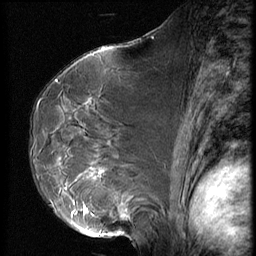
Breast MRI (dynamic contrast-enhanced), one sagittal slice; slice 39 of 62 in the series (ordered by position); 3 images stored at this slice position (order not interpretable as contrast timing); 1.5 T; TE 4.2 ms, TR 9 ms; 2.5 mm slice thickness; 256 × 256 image matrix, field of view 180 × 180 mm. Female patient, age 50 years. From the clinical record (not read from this slice): setting: breast cancer imaged before/during neoadjuvant chemotherapy; receptor status: HR-positive, HER2-negative.
Outlined on this slice (semi-automatically segmented with operator editing):
- analysis volume of interest (the breast-tissue region the enhancement analysis was run in; not a lesion): box from (x=59, y=125) to (x=139, y=238) px
- tumour enhancement mask (voxels above the 140 % enhancement threshold inside the analysis volume of interest): (x=125, y=214)–(x=129, y=217)